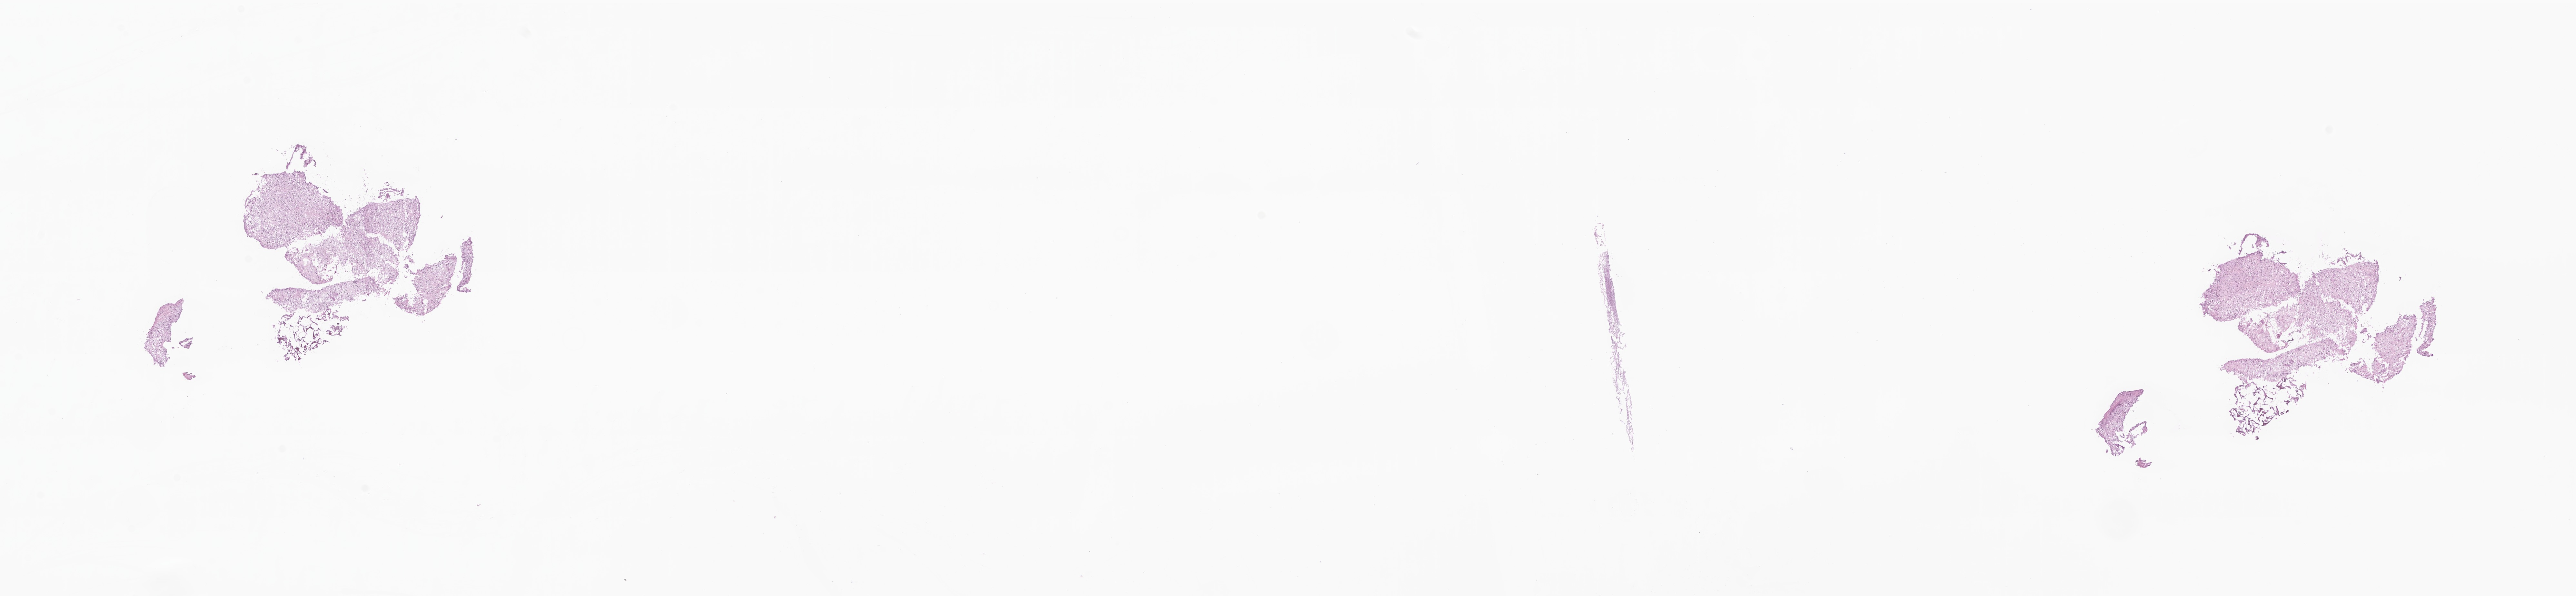
Whole-slide image, H&E stain of tumor tissue from the brain — low-resolution overview of the scanned area, about 33.7 x 7.8 mm, frozen section (OCT-embedded). Patient: female, age 177 months (14 years 9 months).
• diagnosis: Glioma, malignant